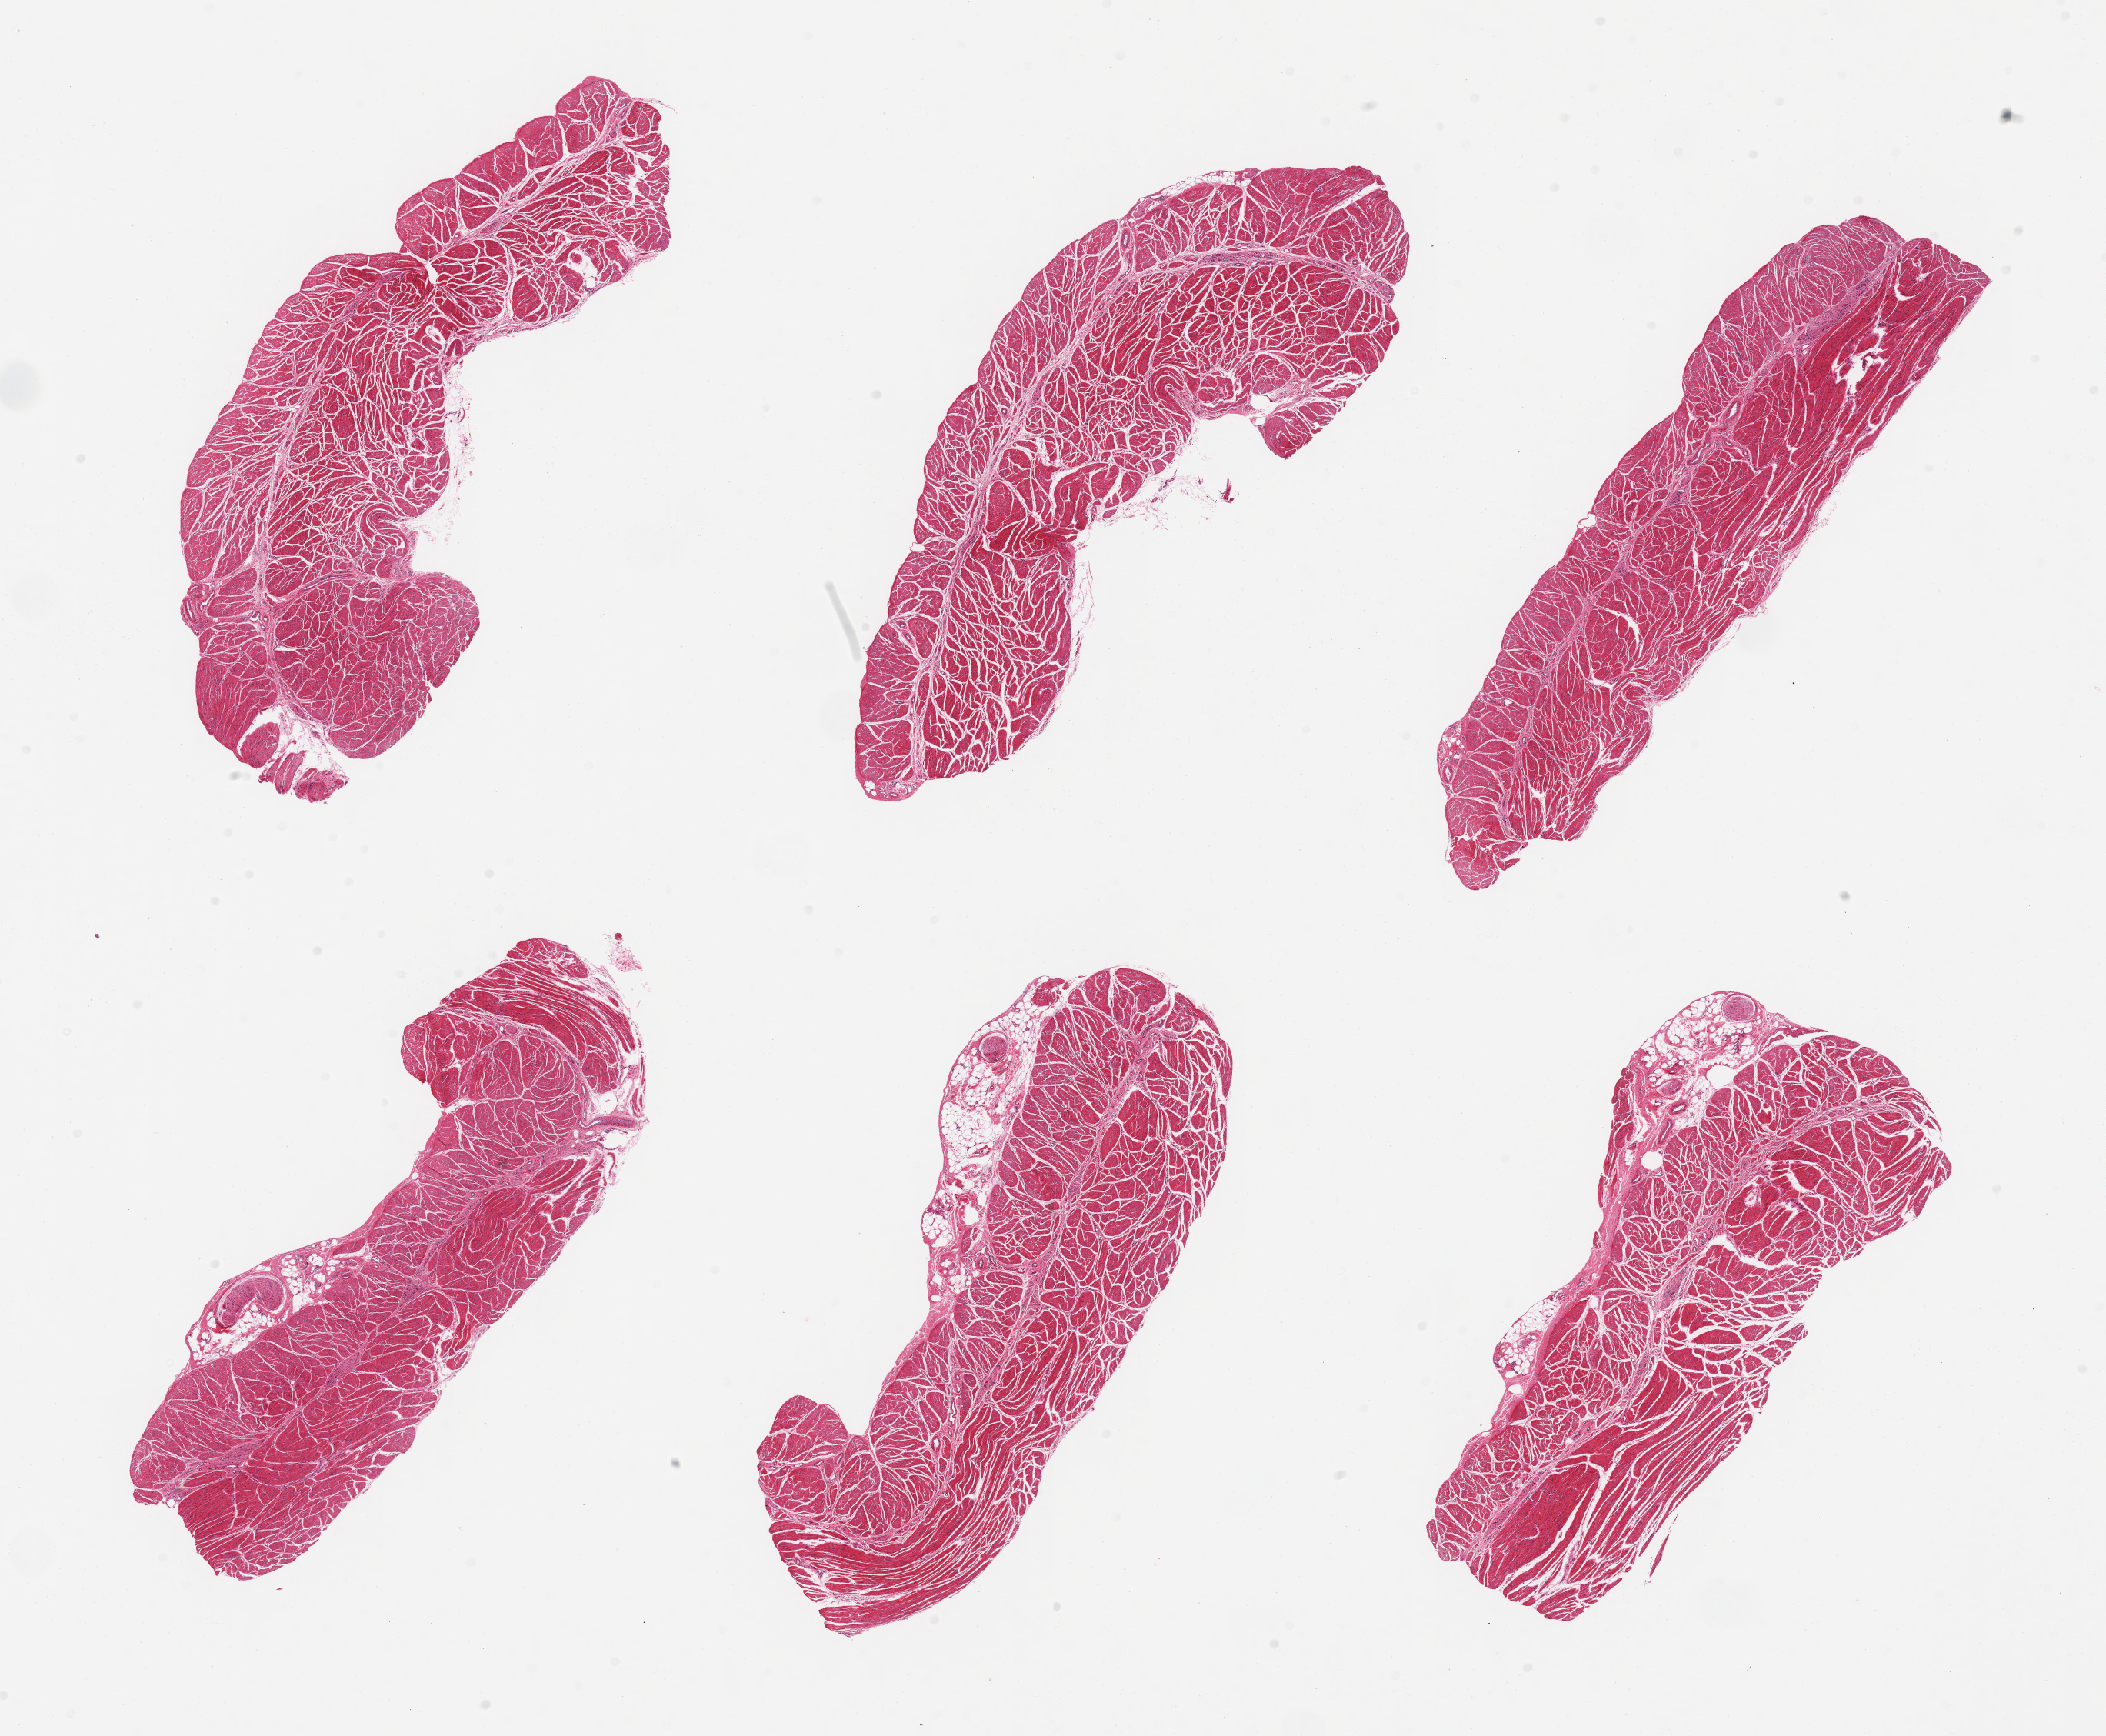
Whole-slide image, H&E stain — a low-resolution overview of the entire scanned area, about 21.7 x 17.9 mm; PAXgene-fixed, paraffin-embedded tissue; sampled site (target tissue): esophageal muscle; donor tissue sample. Donor: male.
- pathologist's review note for this sample: 6 pieces, confirmed target muscularis